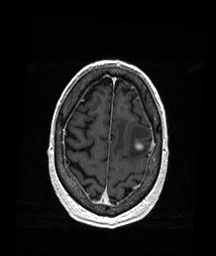
Brain MRI from a brain-tumour surgery series, one axial slice. Position 43 of 176 along the scan axis. T1-weighted post-contrast. 1 mm slice thickness. 216 × 256 image matrix, field of view 211 × 250 mm. From the clinical record (not read from this slice): histopathology: Metastatic Melanoma; tumour location: Left Frontal.
Structures marked on this image (expert manual segmentation):
- tumour: bounding box [x1, y1, x2, y2] px = [134, 140, 143, 151]